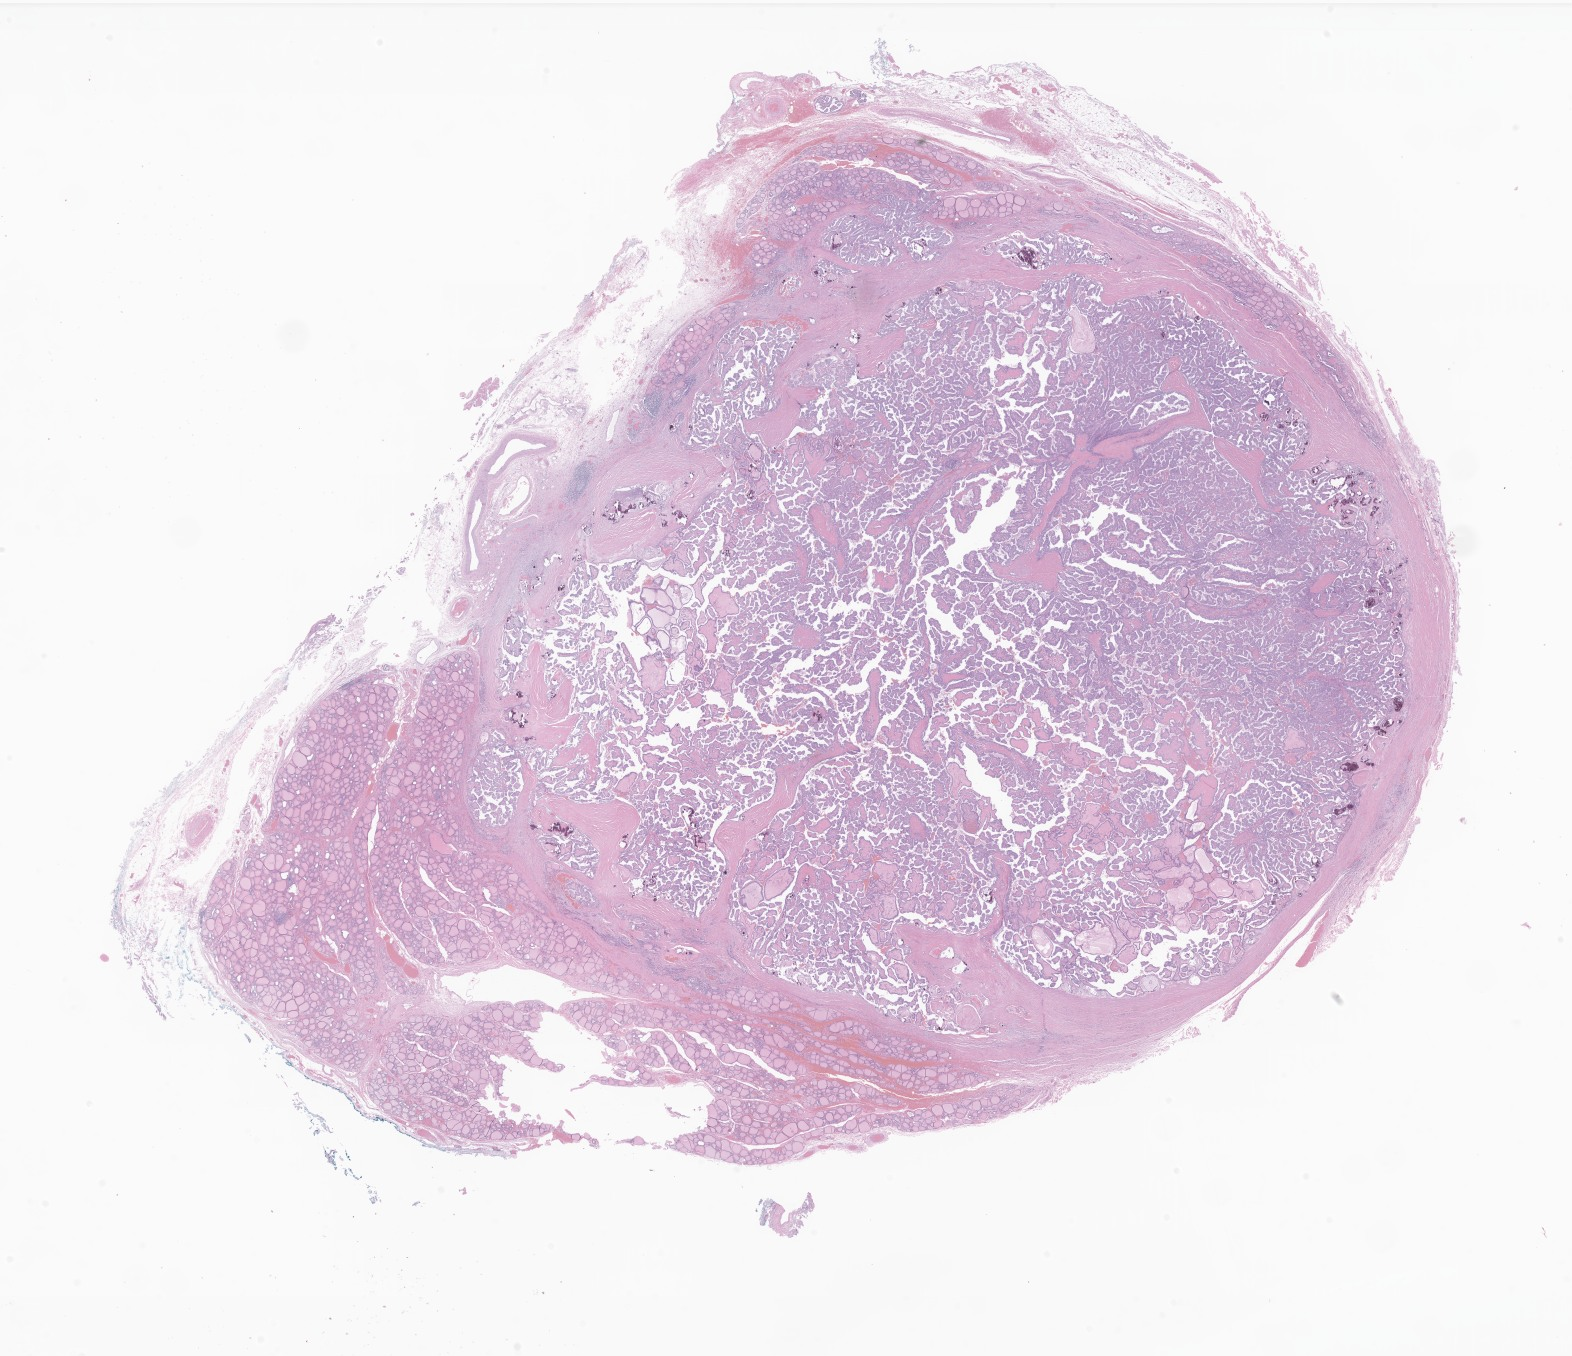
Digitized haematoxylin and eosin-stained section of tumor tissue from the thyroid — whole scanned area (about 26.5 x 22.9 mm) shown as a low-resolution overview, formalin-fixed, paraffin-embedded (FFPE) tissue. Patient: female, age 191 months (15 years 11 months).
Diagnosis (ICD-O-3 morphology term): Papillary carcinoma, NOS.